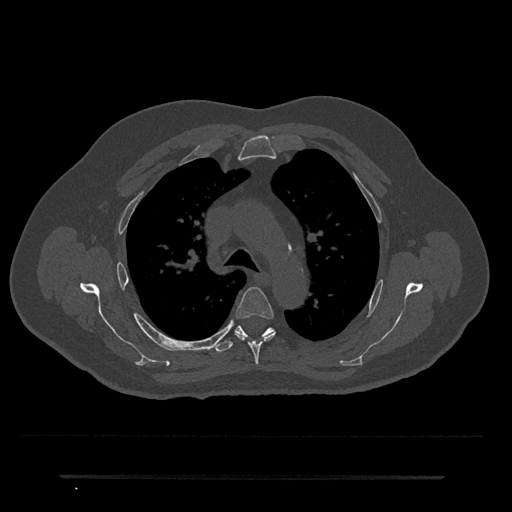
CT including the spine, one axial slice; slice 512 of 797 in the series (ordered by position); reconstruction kernel Br40s/3; 120 kVp; bone window (W 1800 / L 400 HU); 0.5 mm slice thickness; 512 × 512 image matrix, field of view 437 × 437 mm. Male patient, age 69 years. From the clinical record (not read from this slice): primary cancer: prostate.
Annotated regions visible in this slice (semi-automatic segmentation, software-assisted and operator-edited):
- T4 vertebra: bounding box (x1, y1, x2, y2) in pixels: (234, 287, 275, 365)
- T5 vertebra: (213, 326, 274, 353)